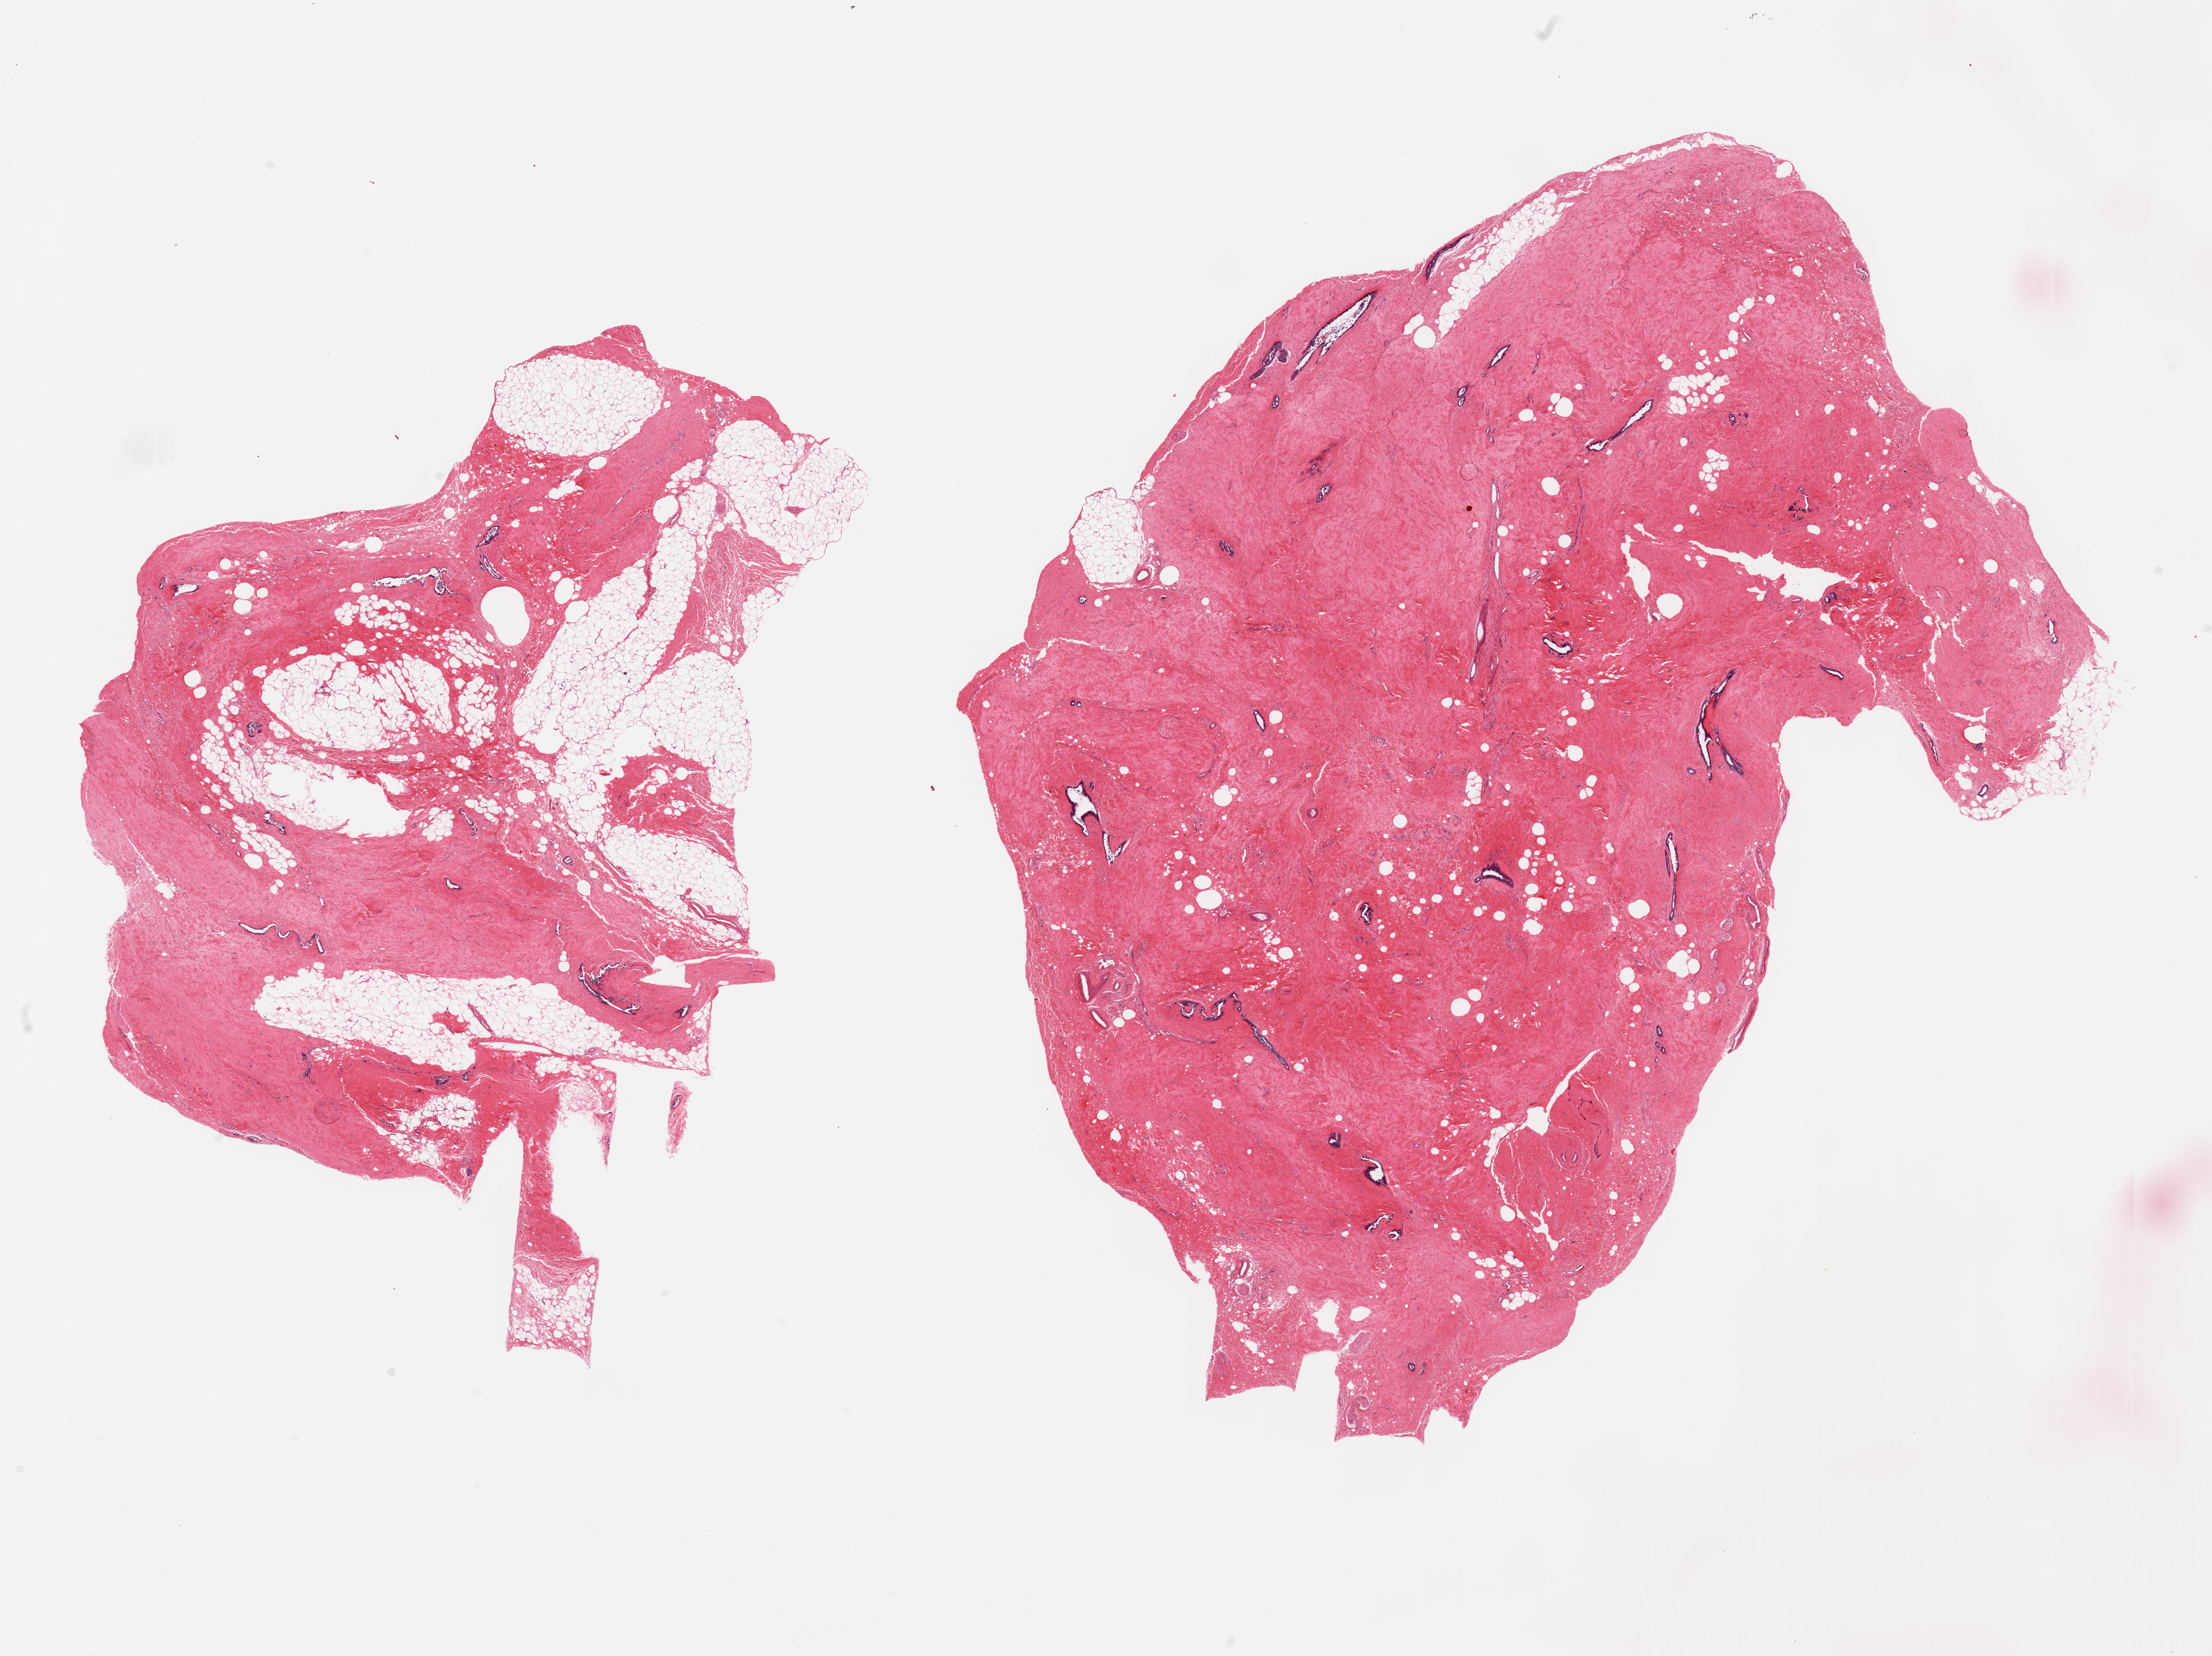
Haematoxylin and eosin whole-slide image, brightfield — shown as a low-resolution overview of the whole scanned area (about 27.6 x 20.6 mm, from a 20x scan), PAXgene-fixed, paraffin-embedded tissue, target tissue: breast, donor tissue sample. Donor sex: male.
Pathologist's review note for this sample: 2 pieces; gynecomastoid changes.